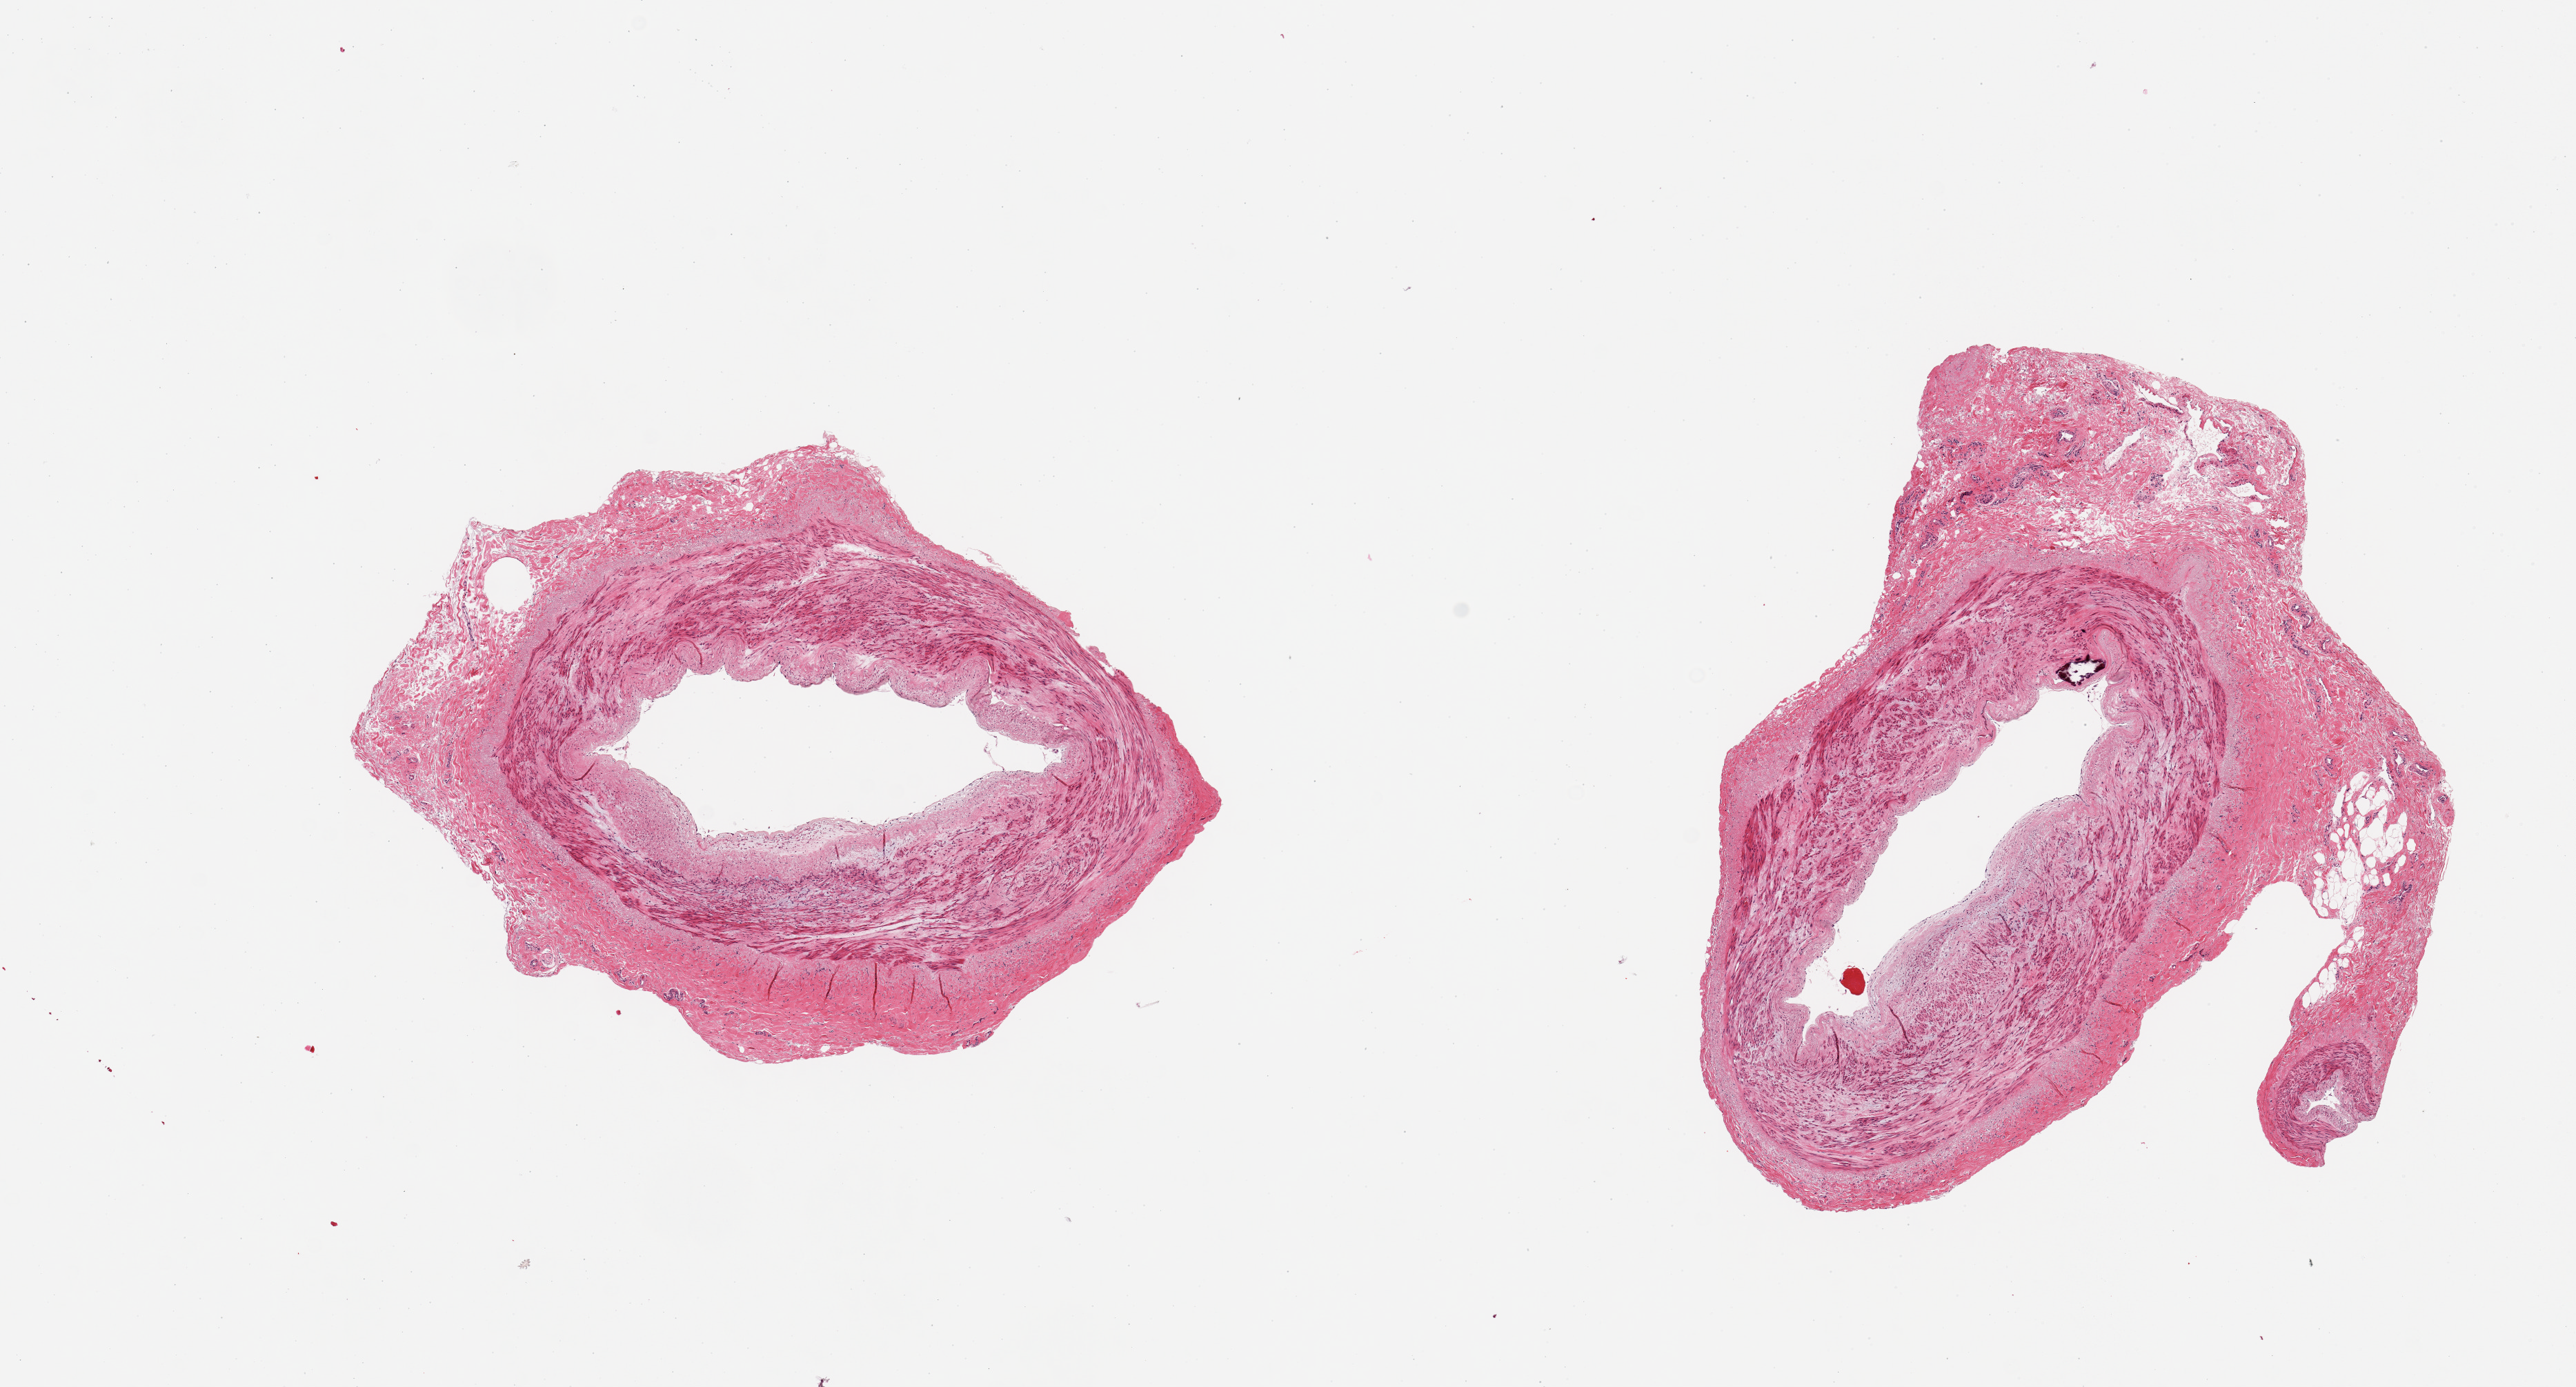
Haematoxylin and eosin whole-slide image, a low-resolution overview of the entire scanned area, about 14.8 x 8.0 mm (from a 20x scan), PAXgene-fixed paraffin-embedded (PFPE) section, section of tibial artery (target tissue), donor tissue sample. Female donor.
• pathologist's review note for this sample: 2 pieces, mild atherosis, focally calcified; rim of fibrous tissue up to ~1.5mm